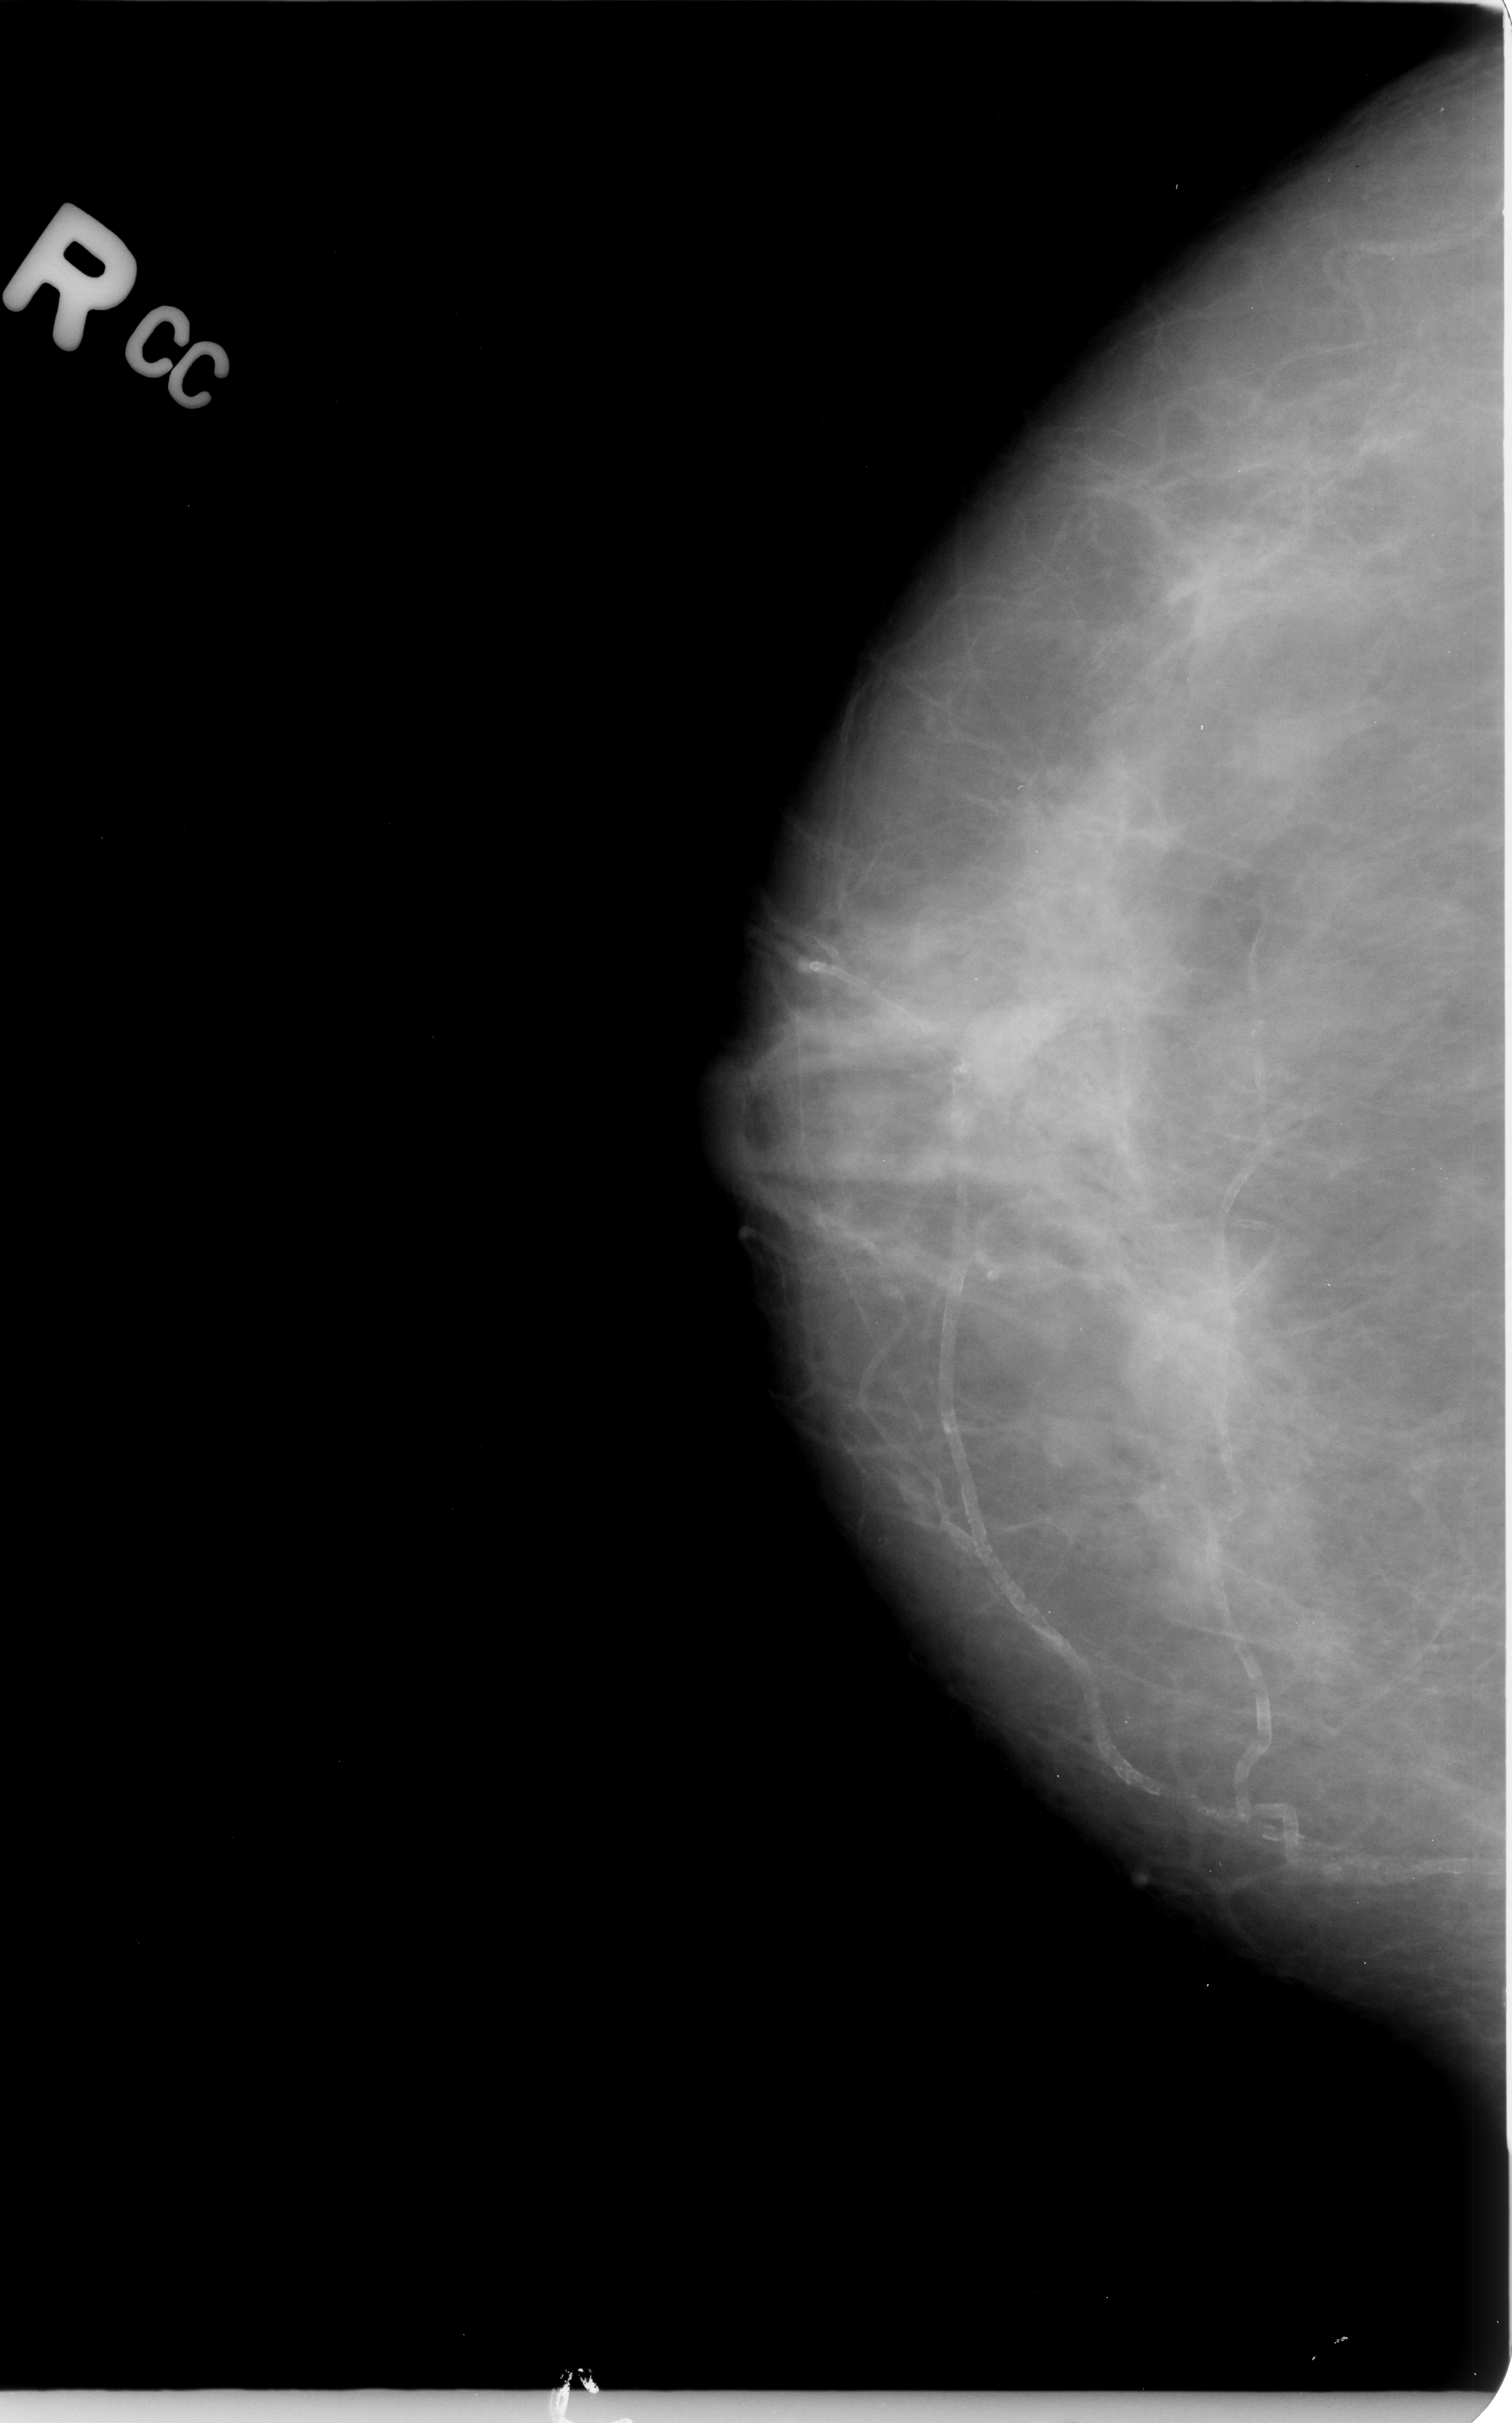
Scanned film-screen mammogram. Right breast. CC view. Breast composition: heterogeneously dense (BI-RADS density category 3 of 4). 1512 × 2423 image matrix.
Expert-marked regions of interest on this film, with their recorded descriptors:
- mass, shape irregular, margins obscured / ill defined; BI-RADS assessment category 4; pathology (as recorded): malignant: bounding box (x1, y1, x2, y2) in pixels: (948, 993, 1065, 1104)